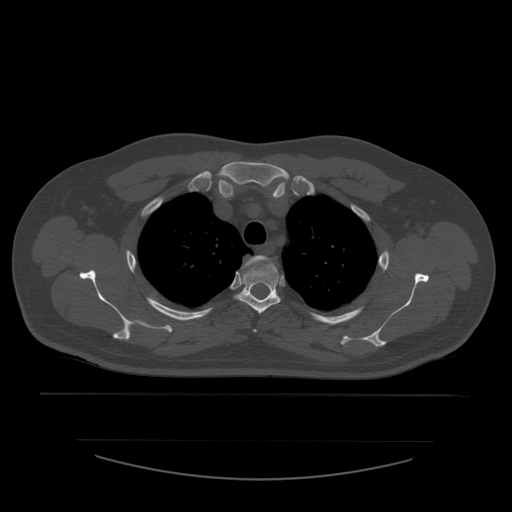
CT including the spine, one axial slice. Slice 436 of 532 in the series (ordered by position). Reconstruction kernel STANDARD. Bone window (W 1800 / L 400 HU). 1.25 mm slice thickness. 512 × 512 image matrix, field of view 441 × 441 mm. Patient age 44 years. Case-level facts recorded for this patient, not image findings: primary cancer: soft tissue sarcoma.
Outlined on this slice (semi-automatically segmented with operator editing):
- T2 vertebra: box from (x=243, y=255) to (x=271, y=332) px
- T3 vertebra: (x=235, y=262)–(x=281, y=315)